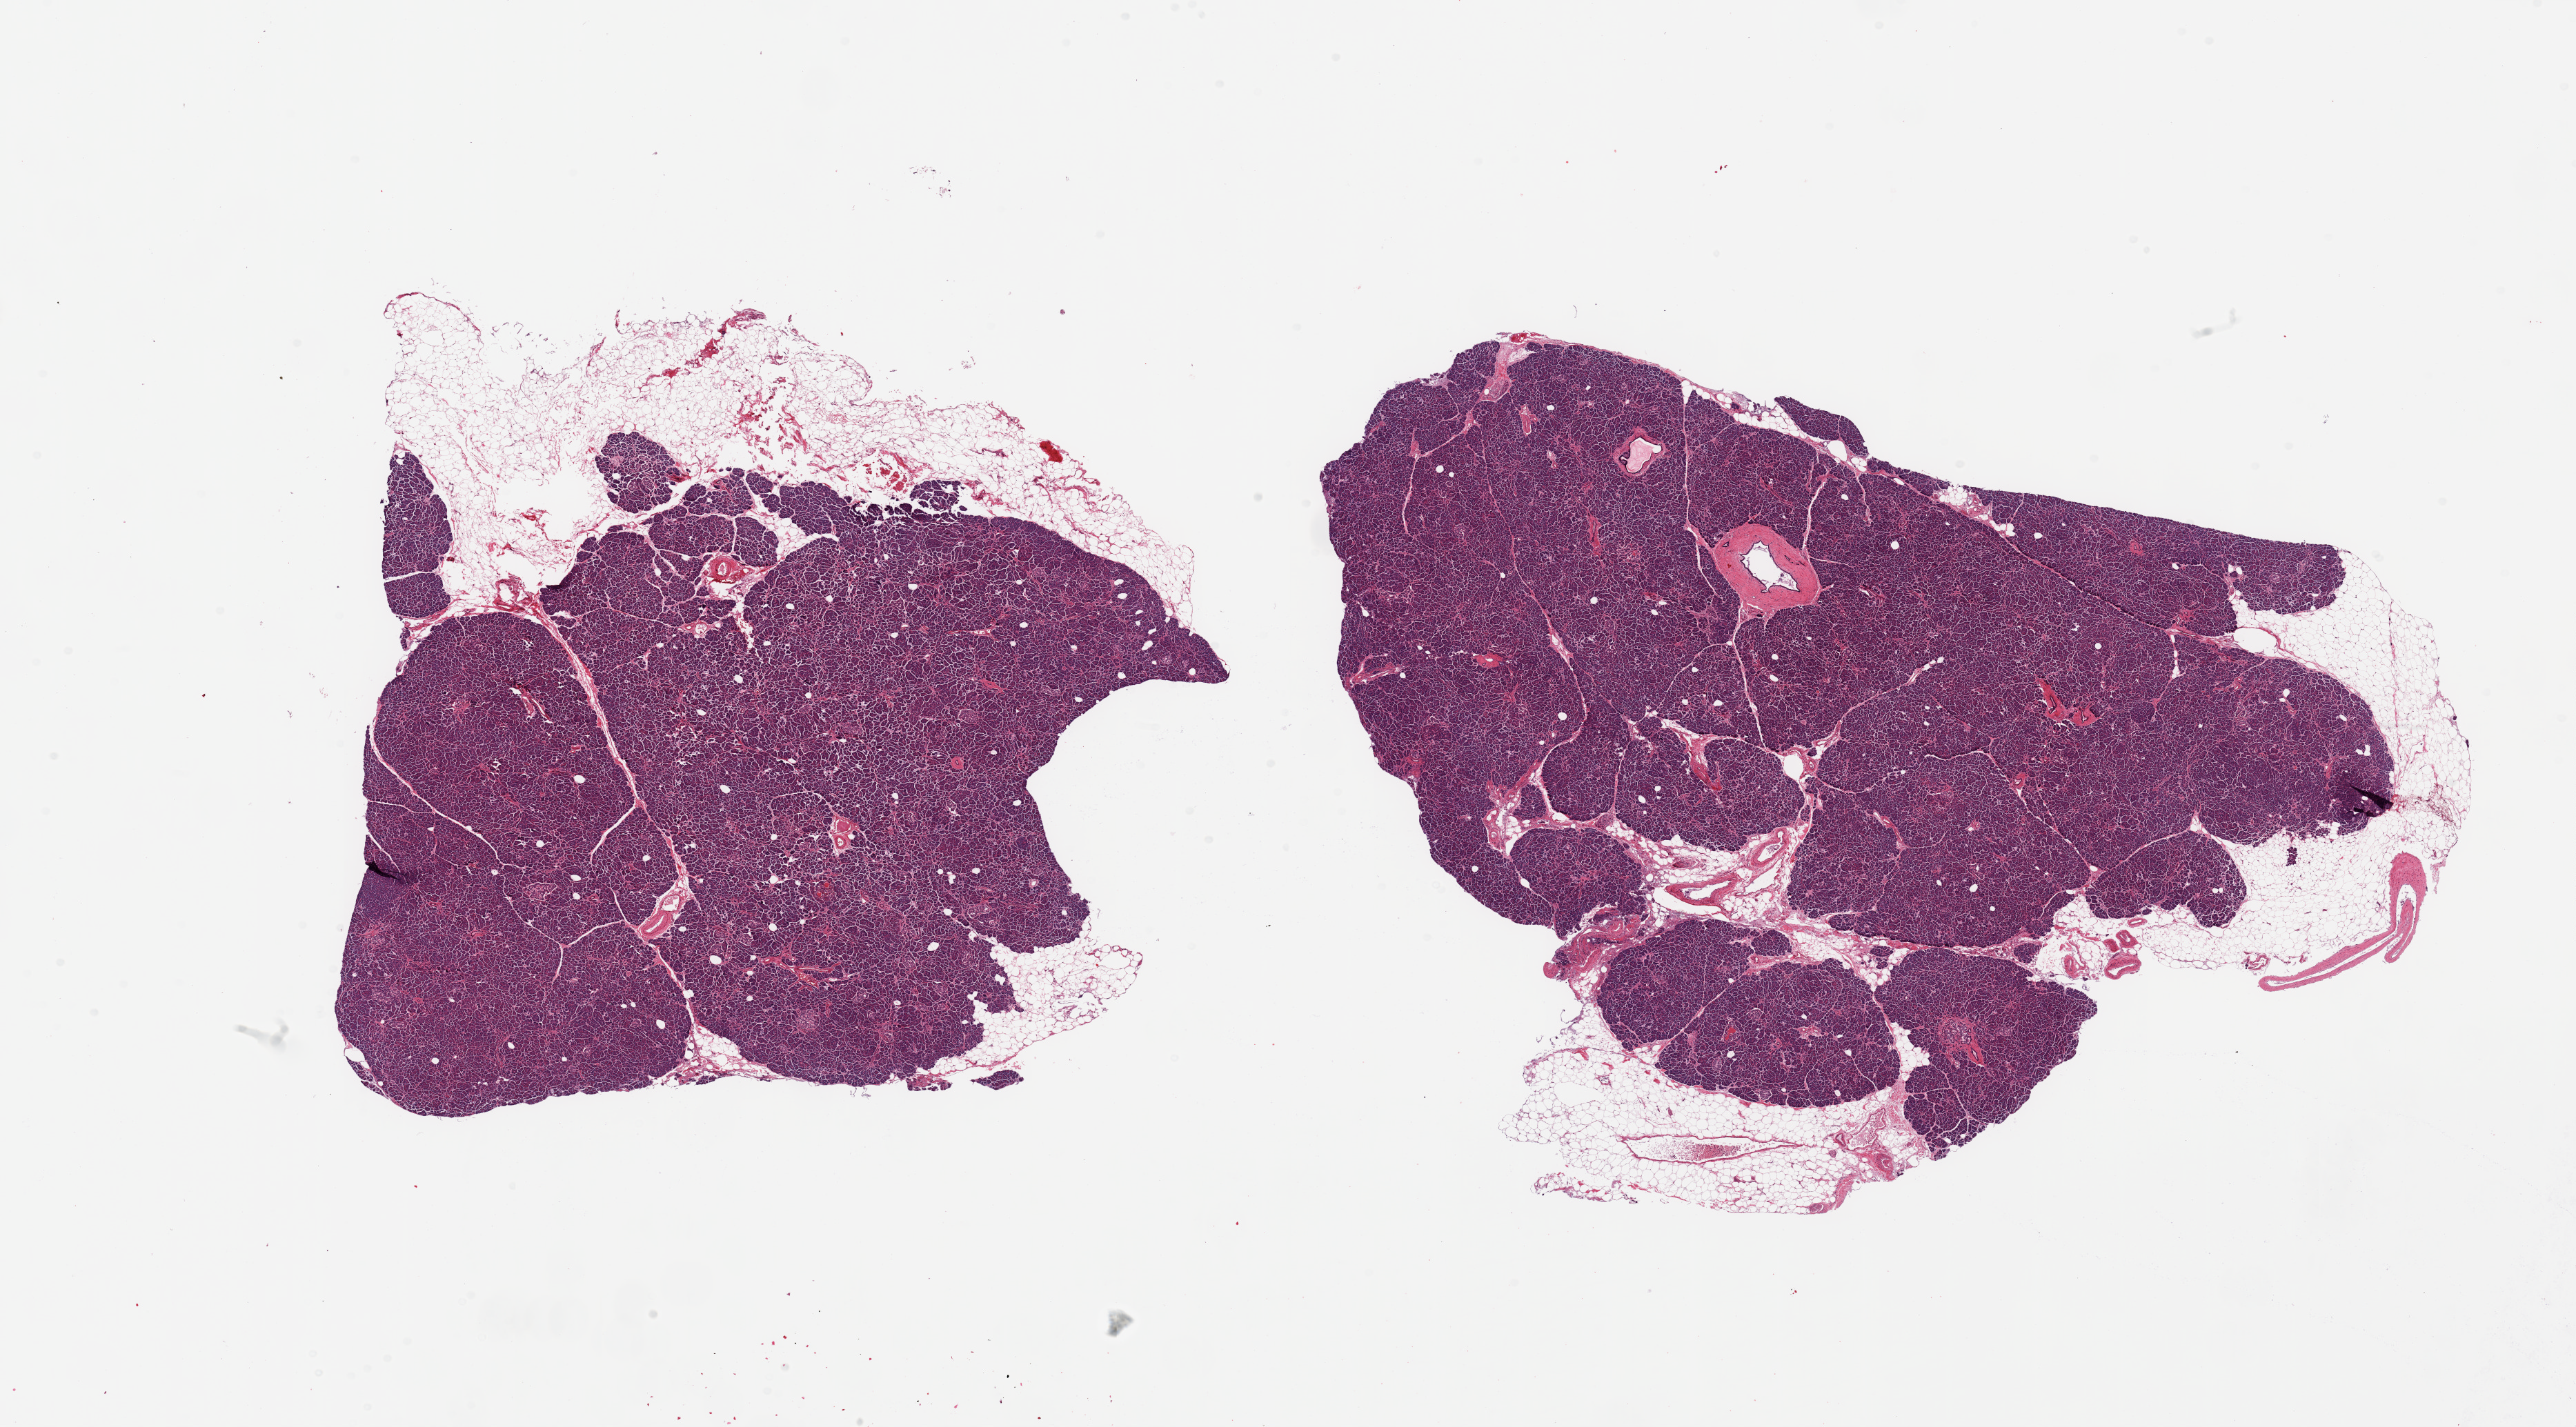
Hematoxylin and eosin (H&E) whole-slide image, a low-resolution overview of the entire scanned area, about 29.5 x 16.4 mm (from a 20x scan). PAXgene-fixed, paraffin-embedded tissue. Section of pancreas (target tissue). Tissue donor sample. Donor sex: male.
• review note (as recorded): 2 pieces; 10-20% attached fat